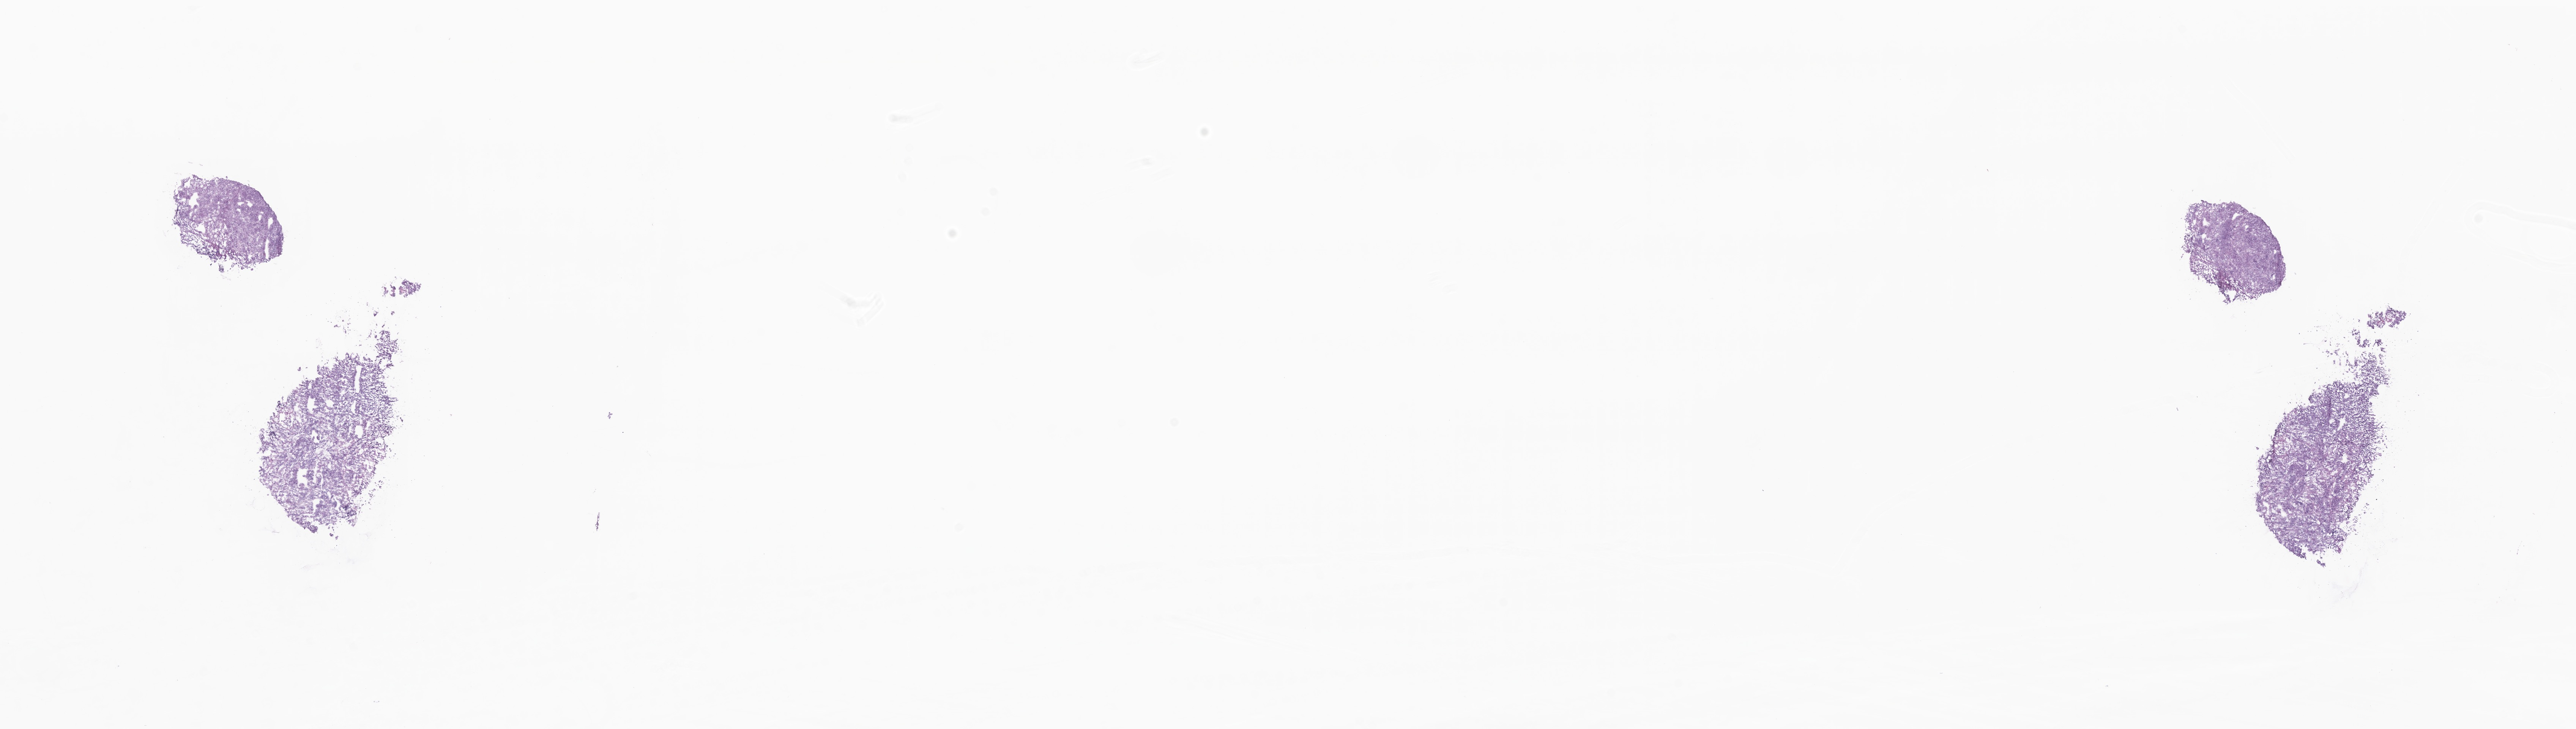
Digitized H&E-stained section, shown as a low-resolution overview of the whole scanned area (about 28.6 x 8.1 mm), frozen section, specimen: primary tumor, site: breast. Female patient; age at initial diagnosis 53 years. Composition of this section per pathologist review: tumor cells 90%, tumor nuclei 90%.
Diagnosis: Infiltrating duct carcinoma, NOS.